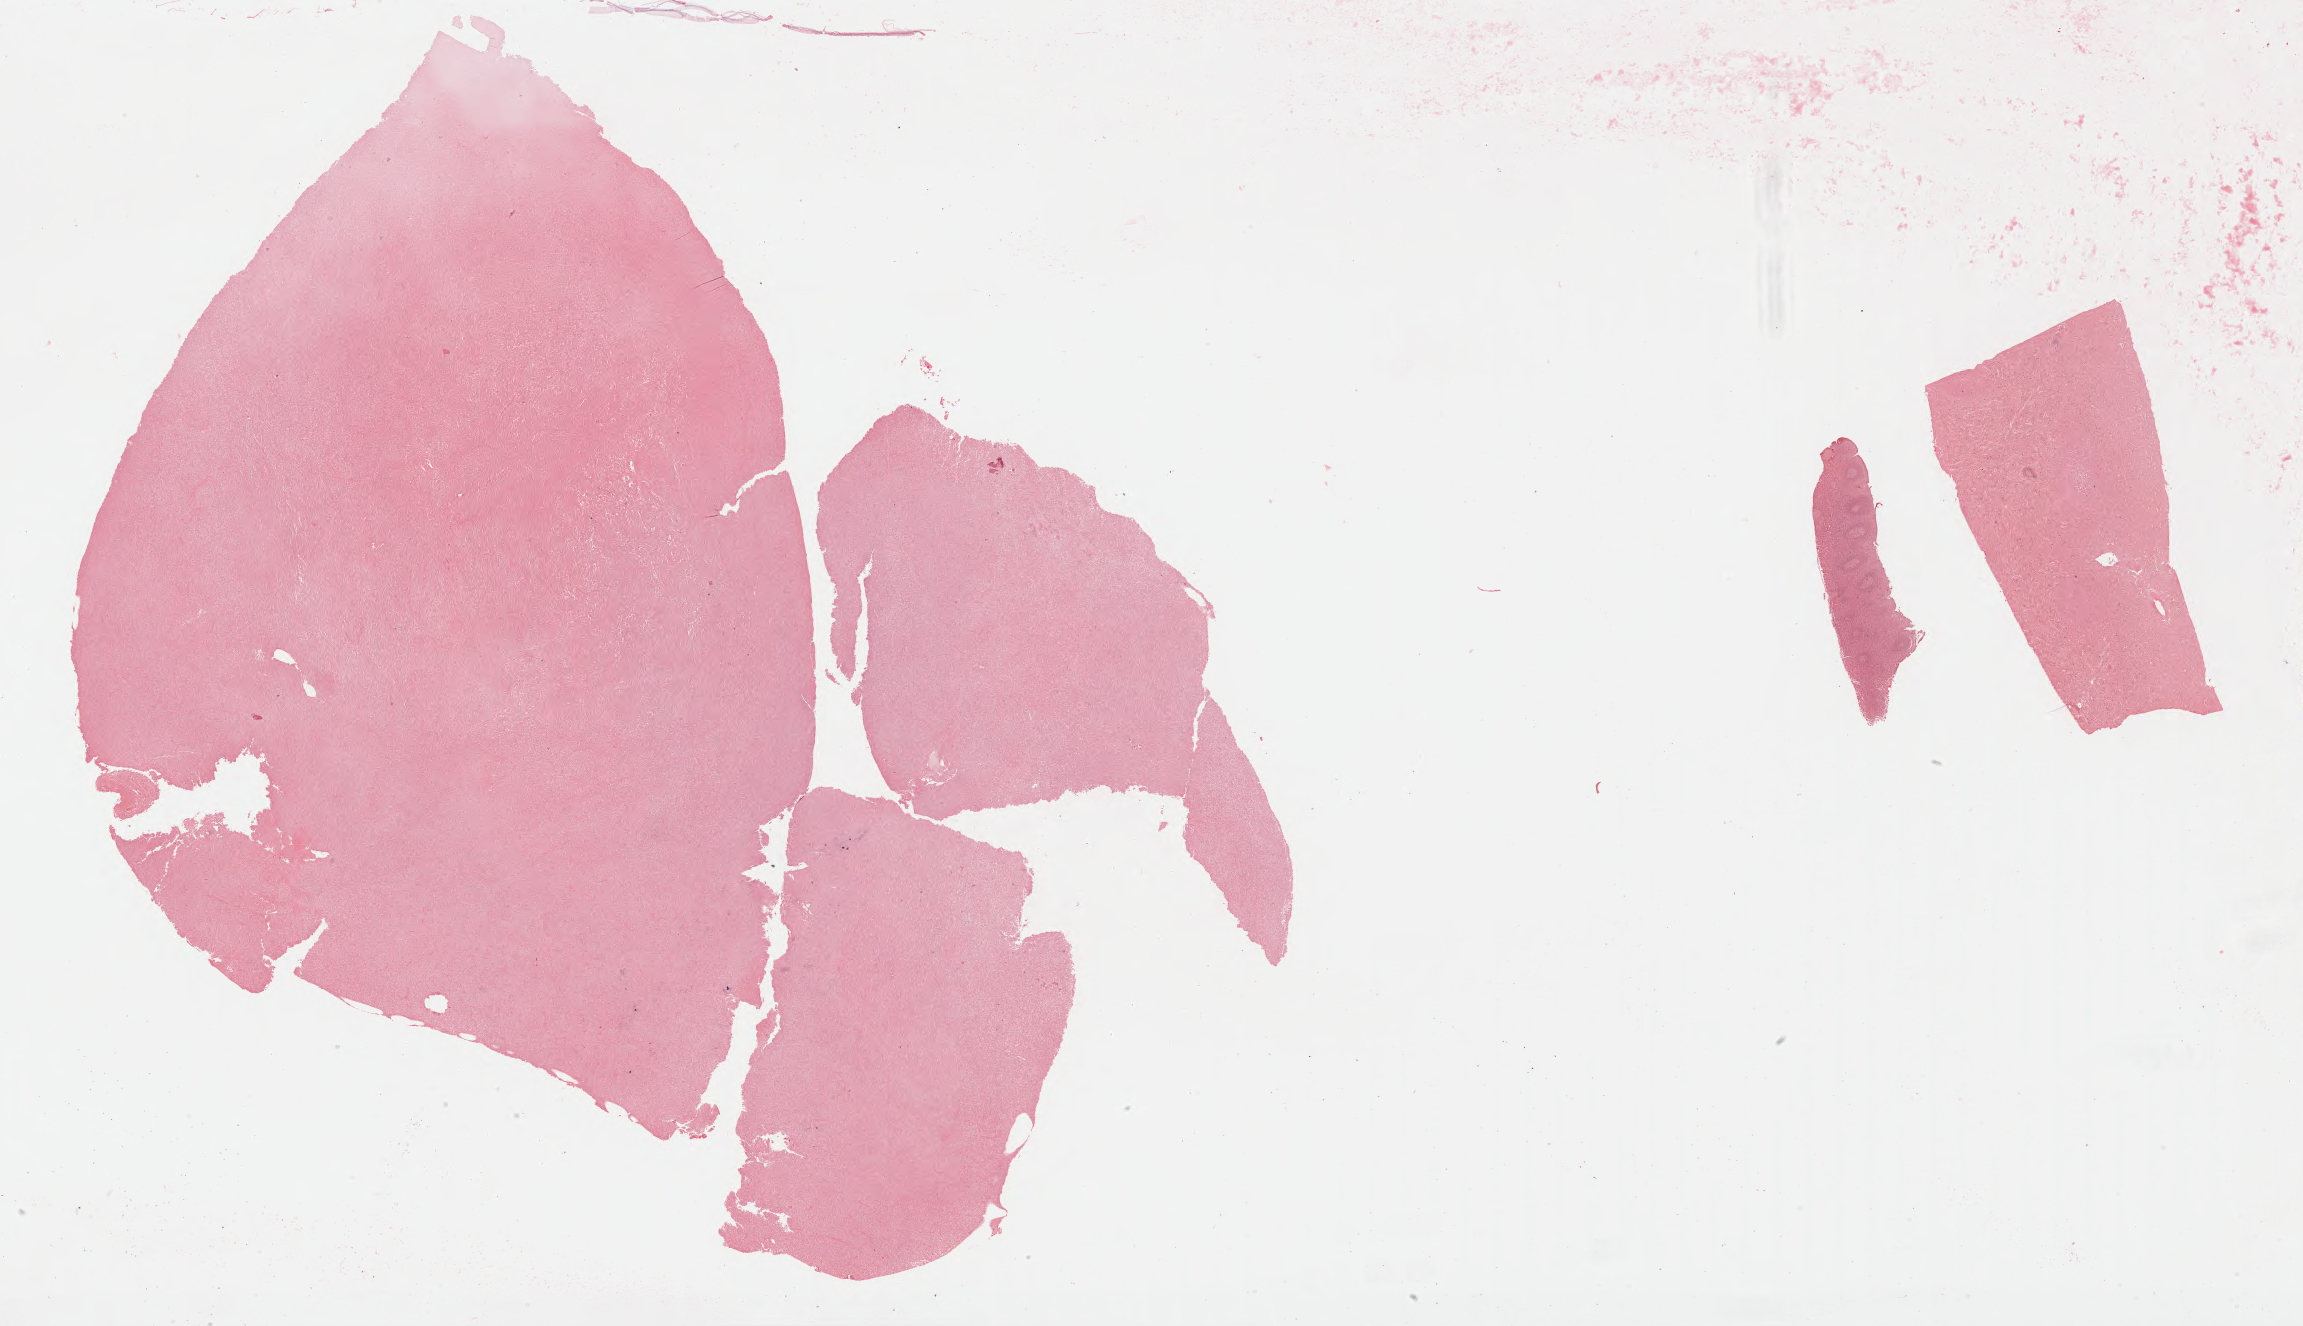
Whole-slide image, Epstein–Barr virus-encoded RNA (EBER) in-situ hybridisation — shown as a low-resolution overview of the whole scanned area (about 37.2 x 21.4 mm). Tumor tissue. Site: liver. Patient female; age 46 years.
* histologic diagnosis: Diffuse large B-cell lymphoma, NOS